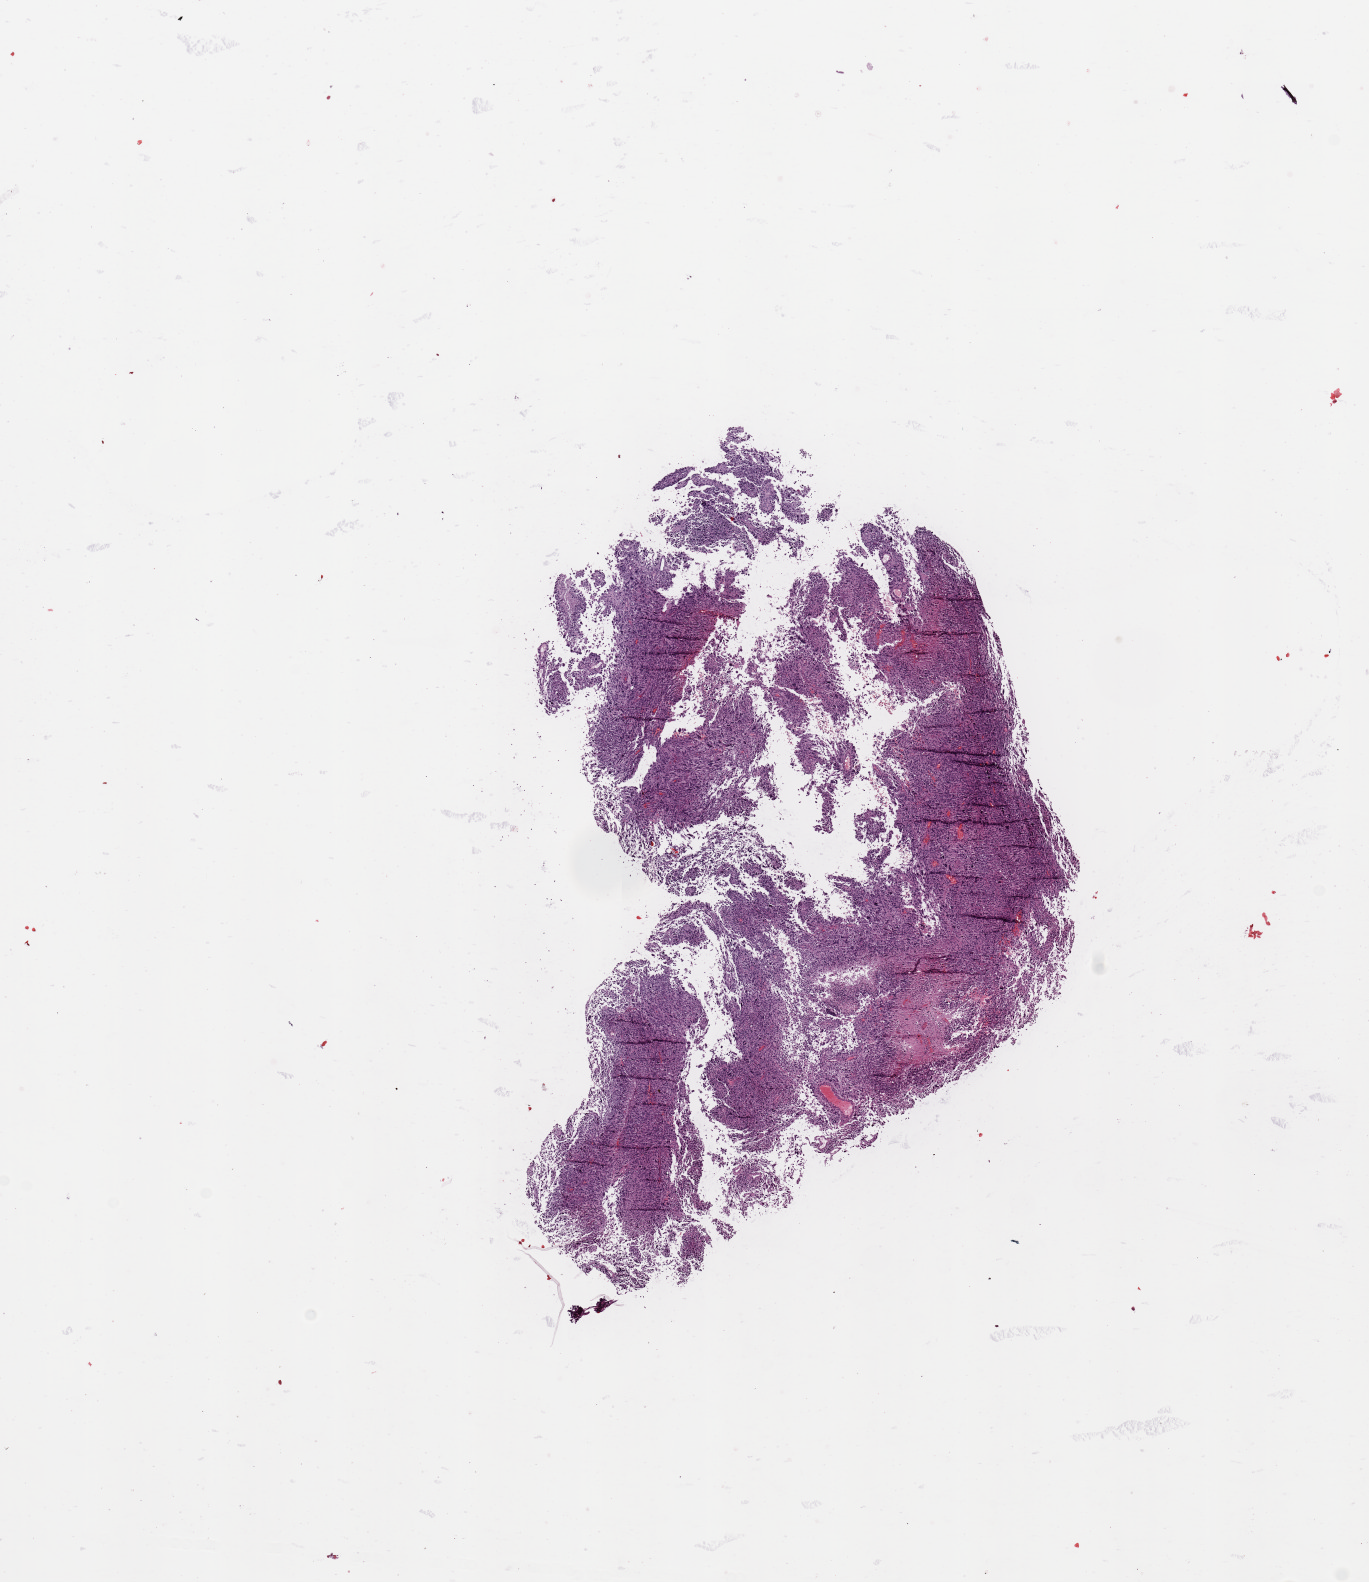
Digitized Hematoxylin and eosin (H&E) stained tissue section (whole slide), low-resolution overview of the scanned area, about 10.8 x 12.5 mm (acquisition: 20x scan). Tumour tissue sample, brain. Patient: female, age 39 years.
Diagnosis: Glioblastoma.